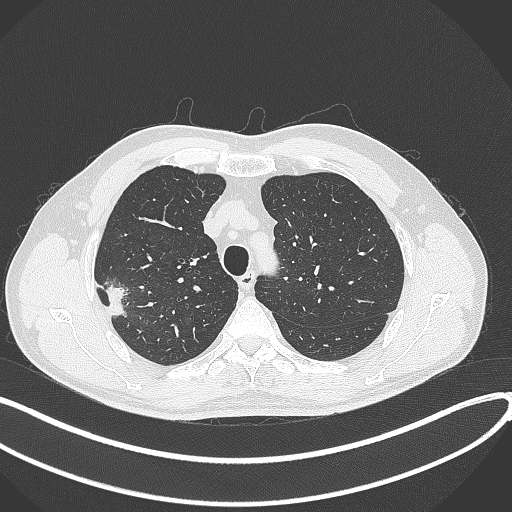
Chest CT, one axial slice. Position 327 of 381 along the scan axis. Lung window (W 1500 / L -600 HU). 1 mm slice thickness. 512 × 512 image matrix, field of view 400 × 400 mm. Male patient, age 62 years. From the clinical record (not read from this slice): clinical TNM (as recorded): T1c N0 M0; histopathological grade: G2-3.
Structures marked on this image (rectangle marked by the reading radiologist):
- lung tumour (recorded histology: adenocarcinoma): bounding box (x1, y1, x2, y2) in pixels: (105, 282, 133, 323)